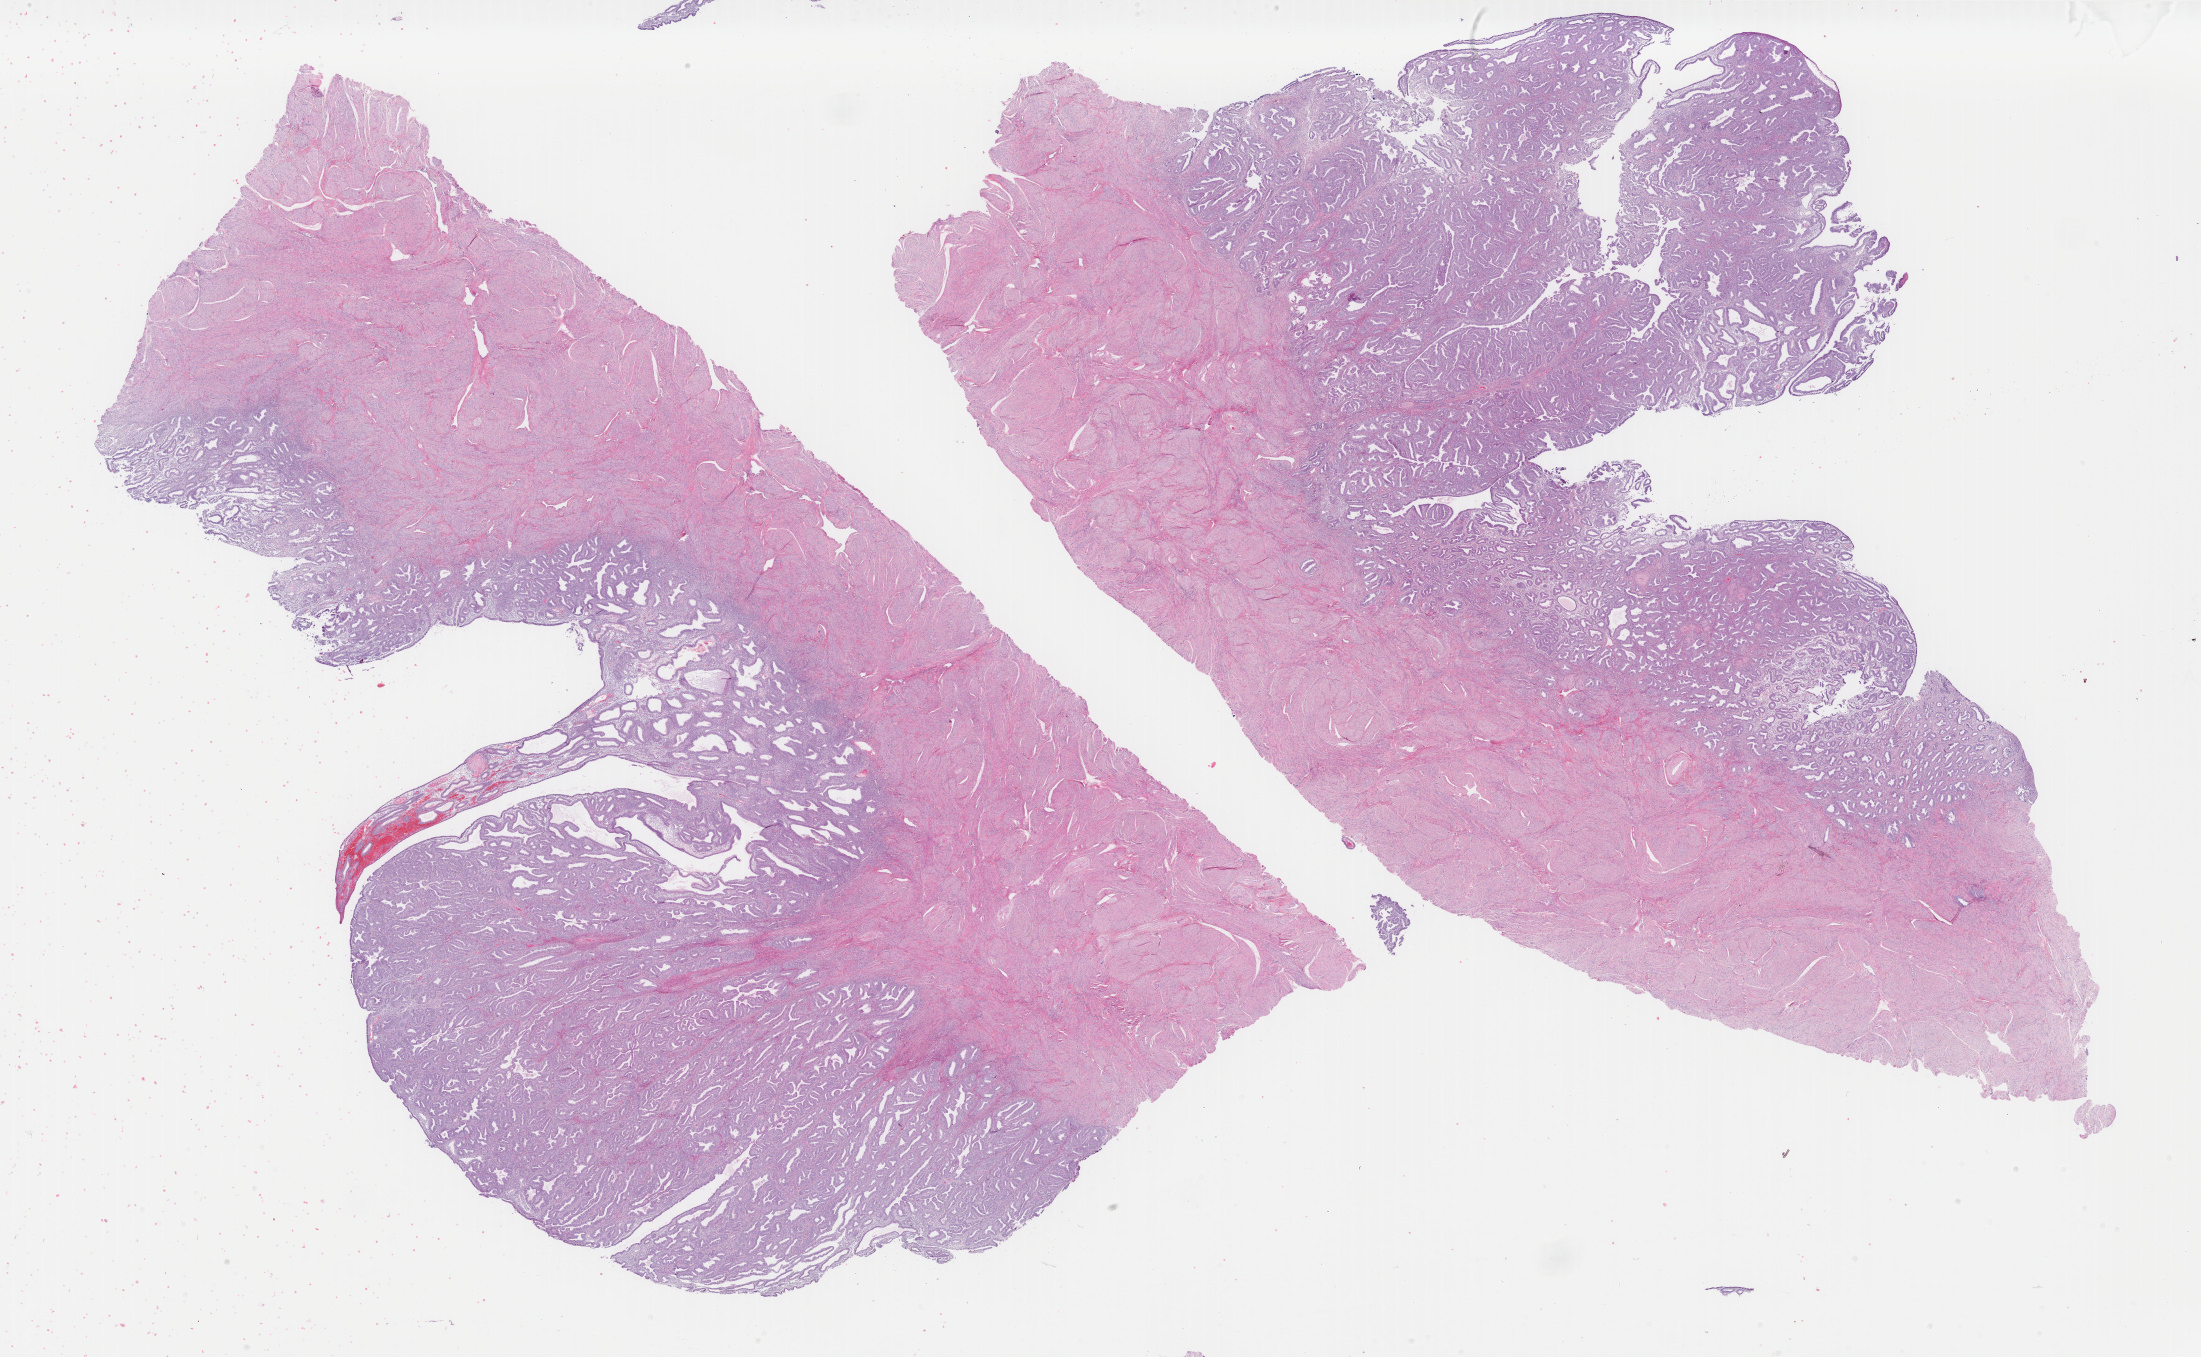
H&E-stained whole-slide image, a low-resolution overview of the entire scanned area, about 34.9 x 21.5 mm, FFPE section, uterus, primary tumour sample. Female patient; age at initial diagnosis 43 years. Histologic grade: G1 (well differentiated).
Diagnosis: Endometrioid adenocarcinoma, NOS (endometrium). FIGO stage: IA.